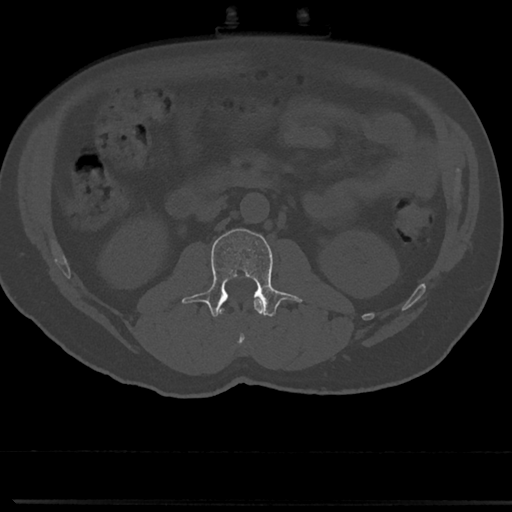
CT including the spine, one axial slice; slice 26 of 817 in the series (ordered by position); reconstruction kernel Br40s/3; bone window (W 1800 / L 400 HU); 0.5 mm slice thickness; 512 × 512 image matrix, field of view 355 × 355 mm. Male patient, age 61 years. Case-level facts recorded for this patient, not image findings: primary cancer: prostate.
Outlined on this slice (semi-automatic segmentation, software-assisted and operator-edited):
- L1 vertebra: bounding box [x1, y1, x2, y2] px = [219, 298, 263, 349]
- L2 vertebra: [191, 228, 300, 318]